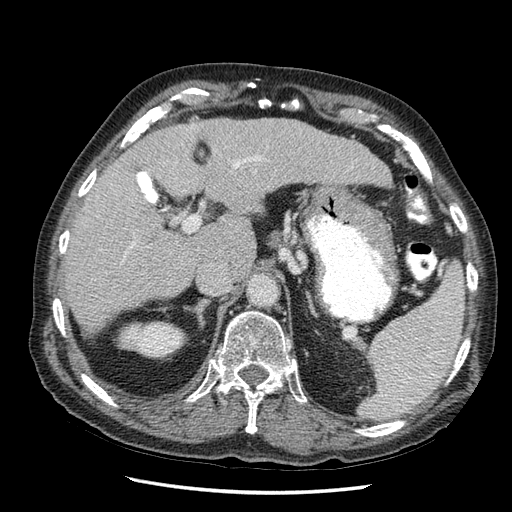
Contrast-enhanced abdominal CT (liver protocol), one axial slice; position 29 of 67 along the scan axis; soft-tissue window (W 400 / L 40 HU); 2.5 mm slice thickness; 512 × 512 image matrix, field of view 360 × 360 mm. Case-level facts recorded for this patient, not image findings: diagnosis: hepatocellular carcinoma (patient treated with transarterial chemoembolisation; whether this scan precedes or follows treatment is not stated here); TNM stage (as recorded): Stage-I; Child-Pugh class: A; tumour differentiation: moderately differentiated; tumour nodularity: uninodular.
Annotated regions visible in this slice (semi-automatic segmentation, software-assisted and operator-edited):
- liver parenchyma outside the tumour (the mass and vessels are separate outlines, so this box may not span the whole liver): box from (x=64, y=116) to (x=392, y=324) px
- liver vessels: (x=128, y=162)–(x=247, y=254)